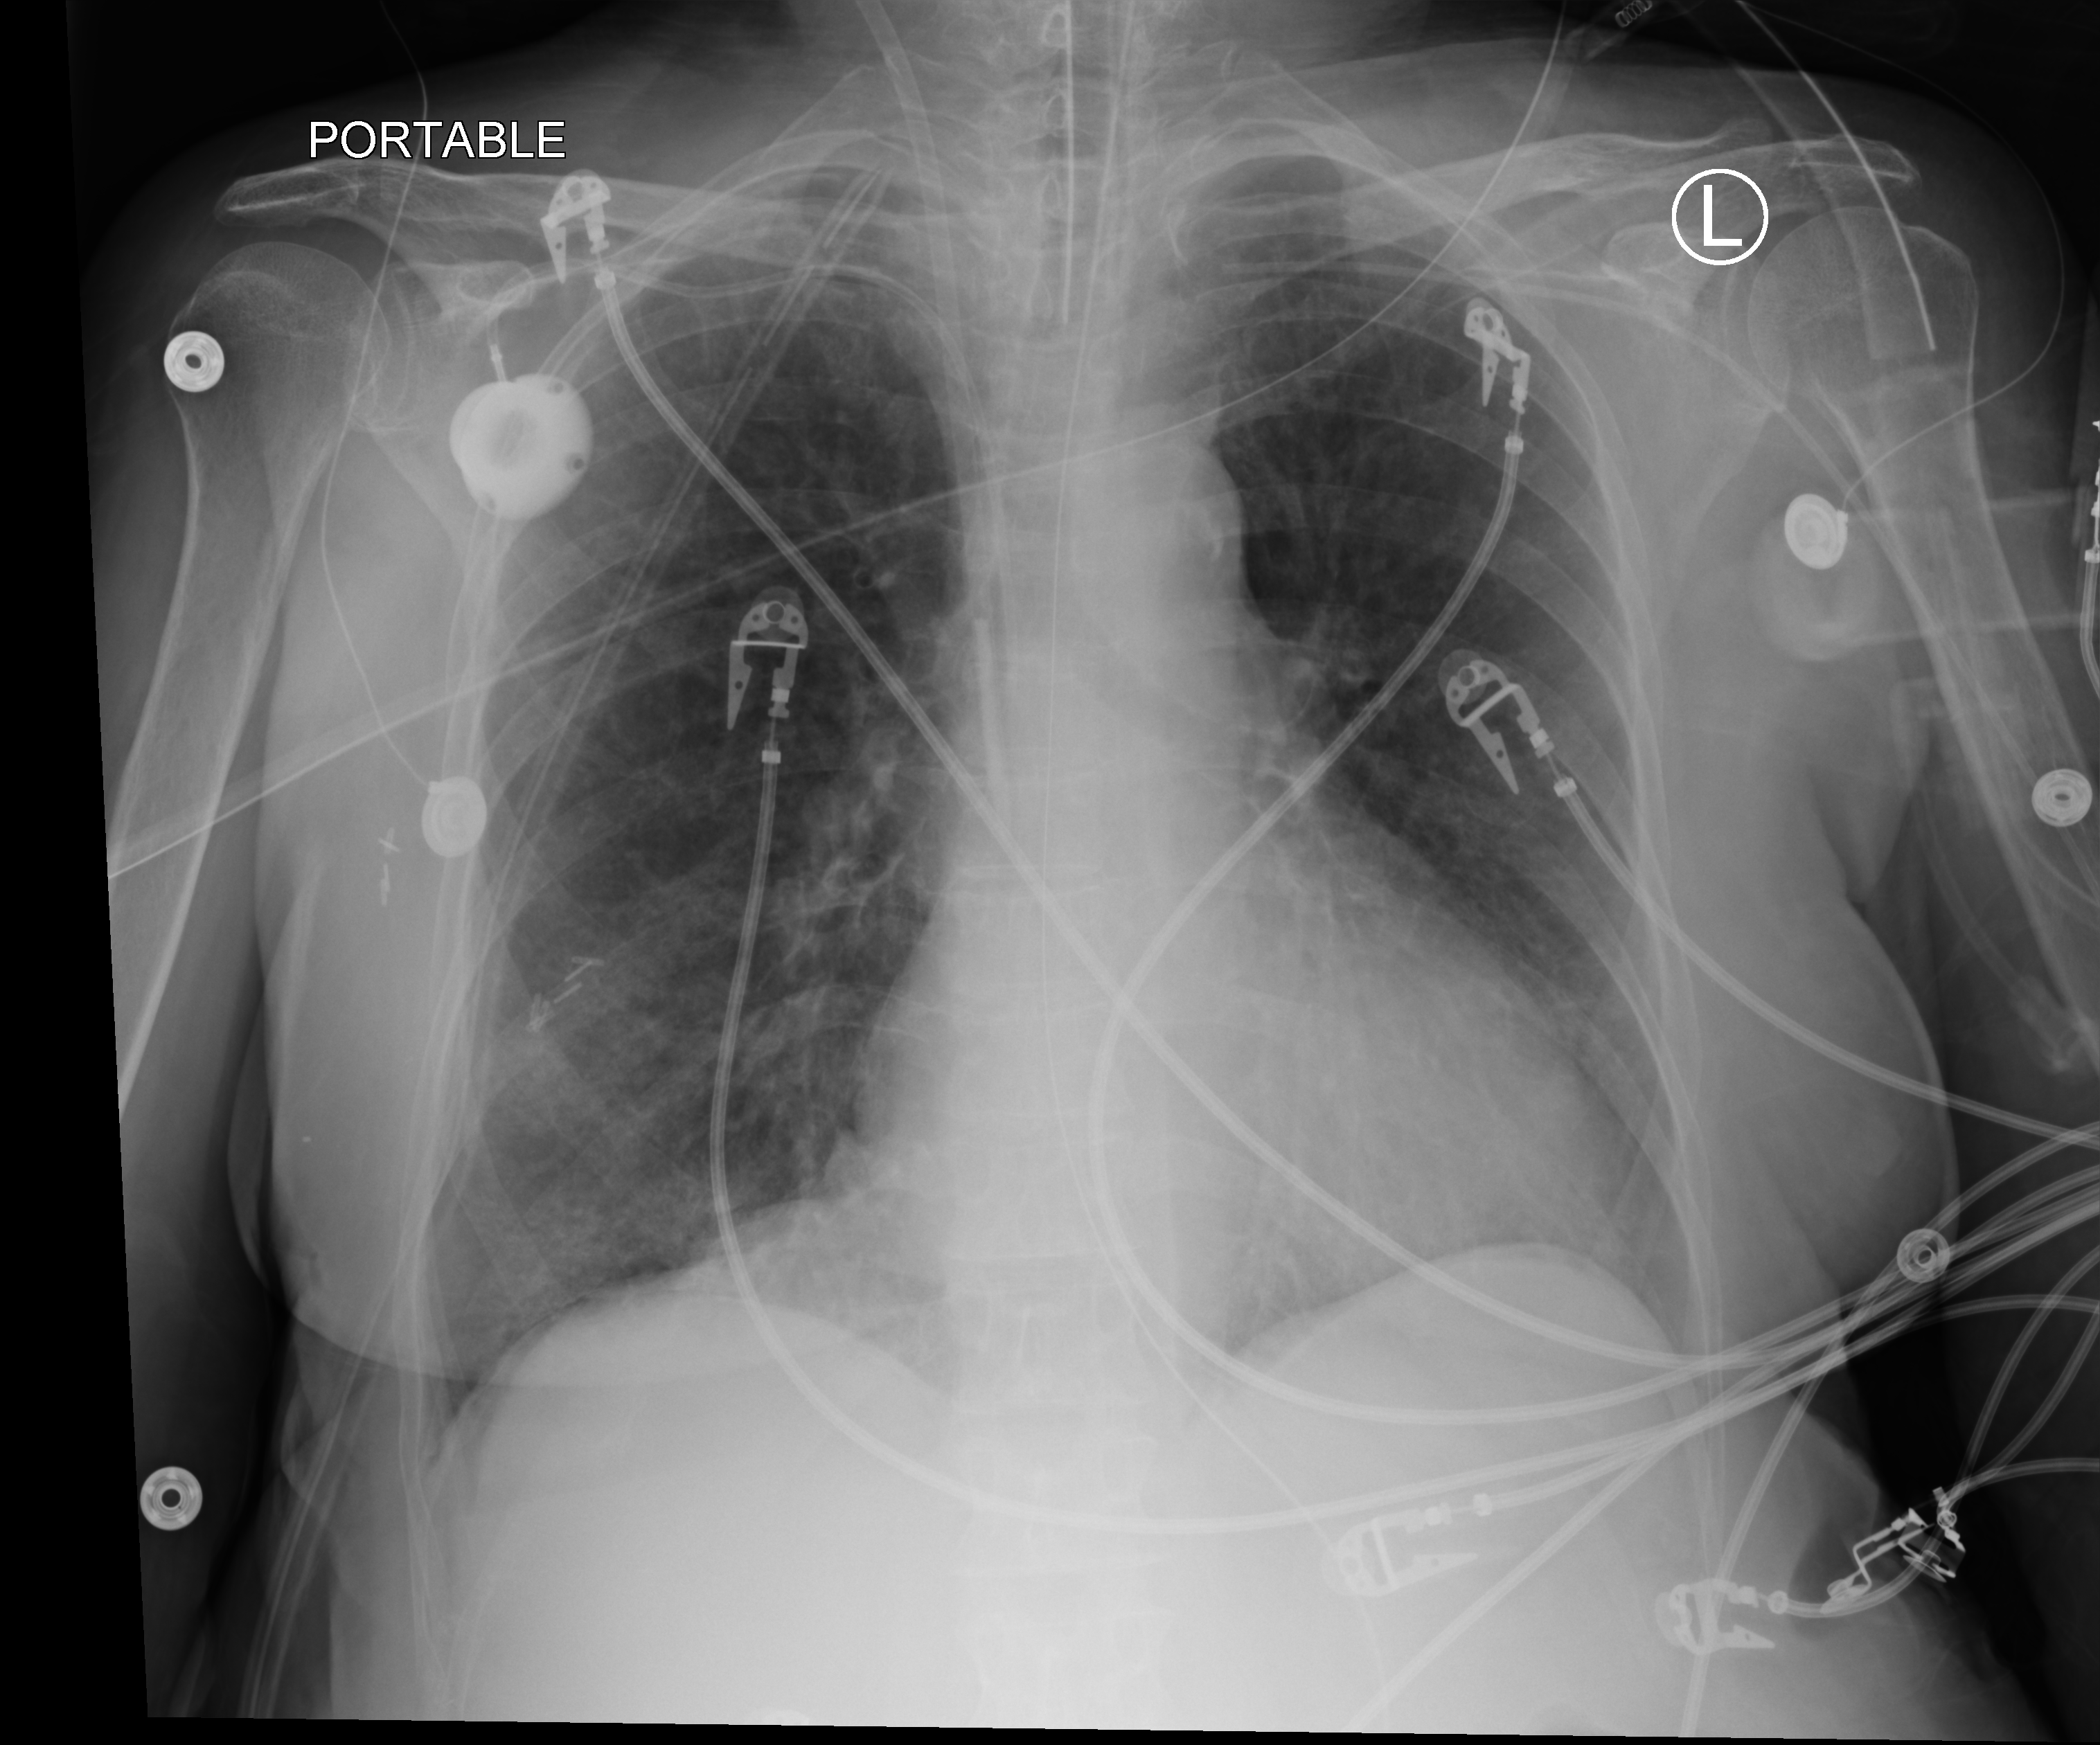
Chest X-ray (portable). Female patient hospitalised with COVID-19, age 60–74 years.
Hospital-stay facts (about this admission, not read from this image; timing relative to this image not recorded): mechanically ventilated during this hospital stay: yes.